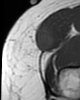
MRI of an extremity soft-tissue mass, one axial slice; MR volume resampled by the dataset authors to the PET/CT grid (not the native acquisition matrix); 3.27 mm slice thickness; 80 × 100 image matrix, field of view 78 × 98 mm. Female patient. From the clinical record (not read from this slice): histological type: synovial sarcoma; grade: intermediate; site of the primary tumour: right thigh.
Annotated regions visible in this slice (expert contour drawn on MRI and transferred to this co-registered scan by the dataset authors):
- gross tumour volume including surrounding oedema: bounding box (x1, y1, x2, y2) in pixels: (35, 28, 54, 50)
- gross tumour volume (mass): (35, 28, 54, 52)